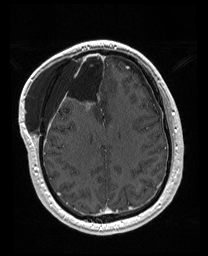
Brain MRI from a brain-tumour surgery series, one axial slice. Position 66 of 176 along the scan axis. T1-weighted post-contrast. 1 mm slice thickness. 208 × 256 image matrix, field of view 208 × 256 mm. Case-level facts recorded for this patient, not image findings: histopathology: Astrocytoma; WHO grade: 4; IDH mutation: yes.
Annotated regions visible in this slice (manually delineated by an expert):
- previous resection cavity: box from (x=61, y=52) to (x=98, y=111) px